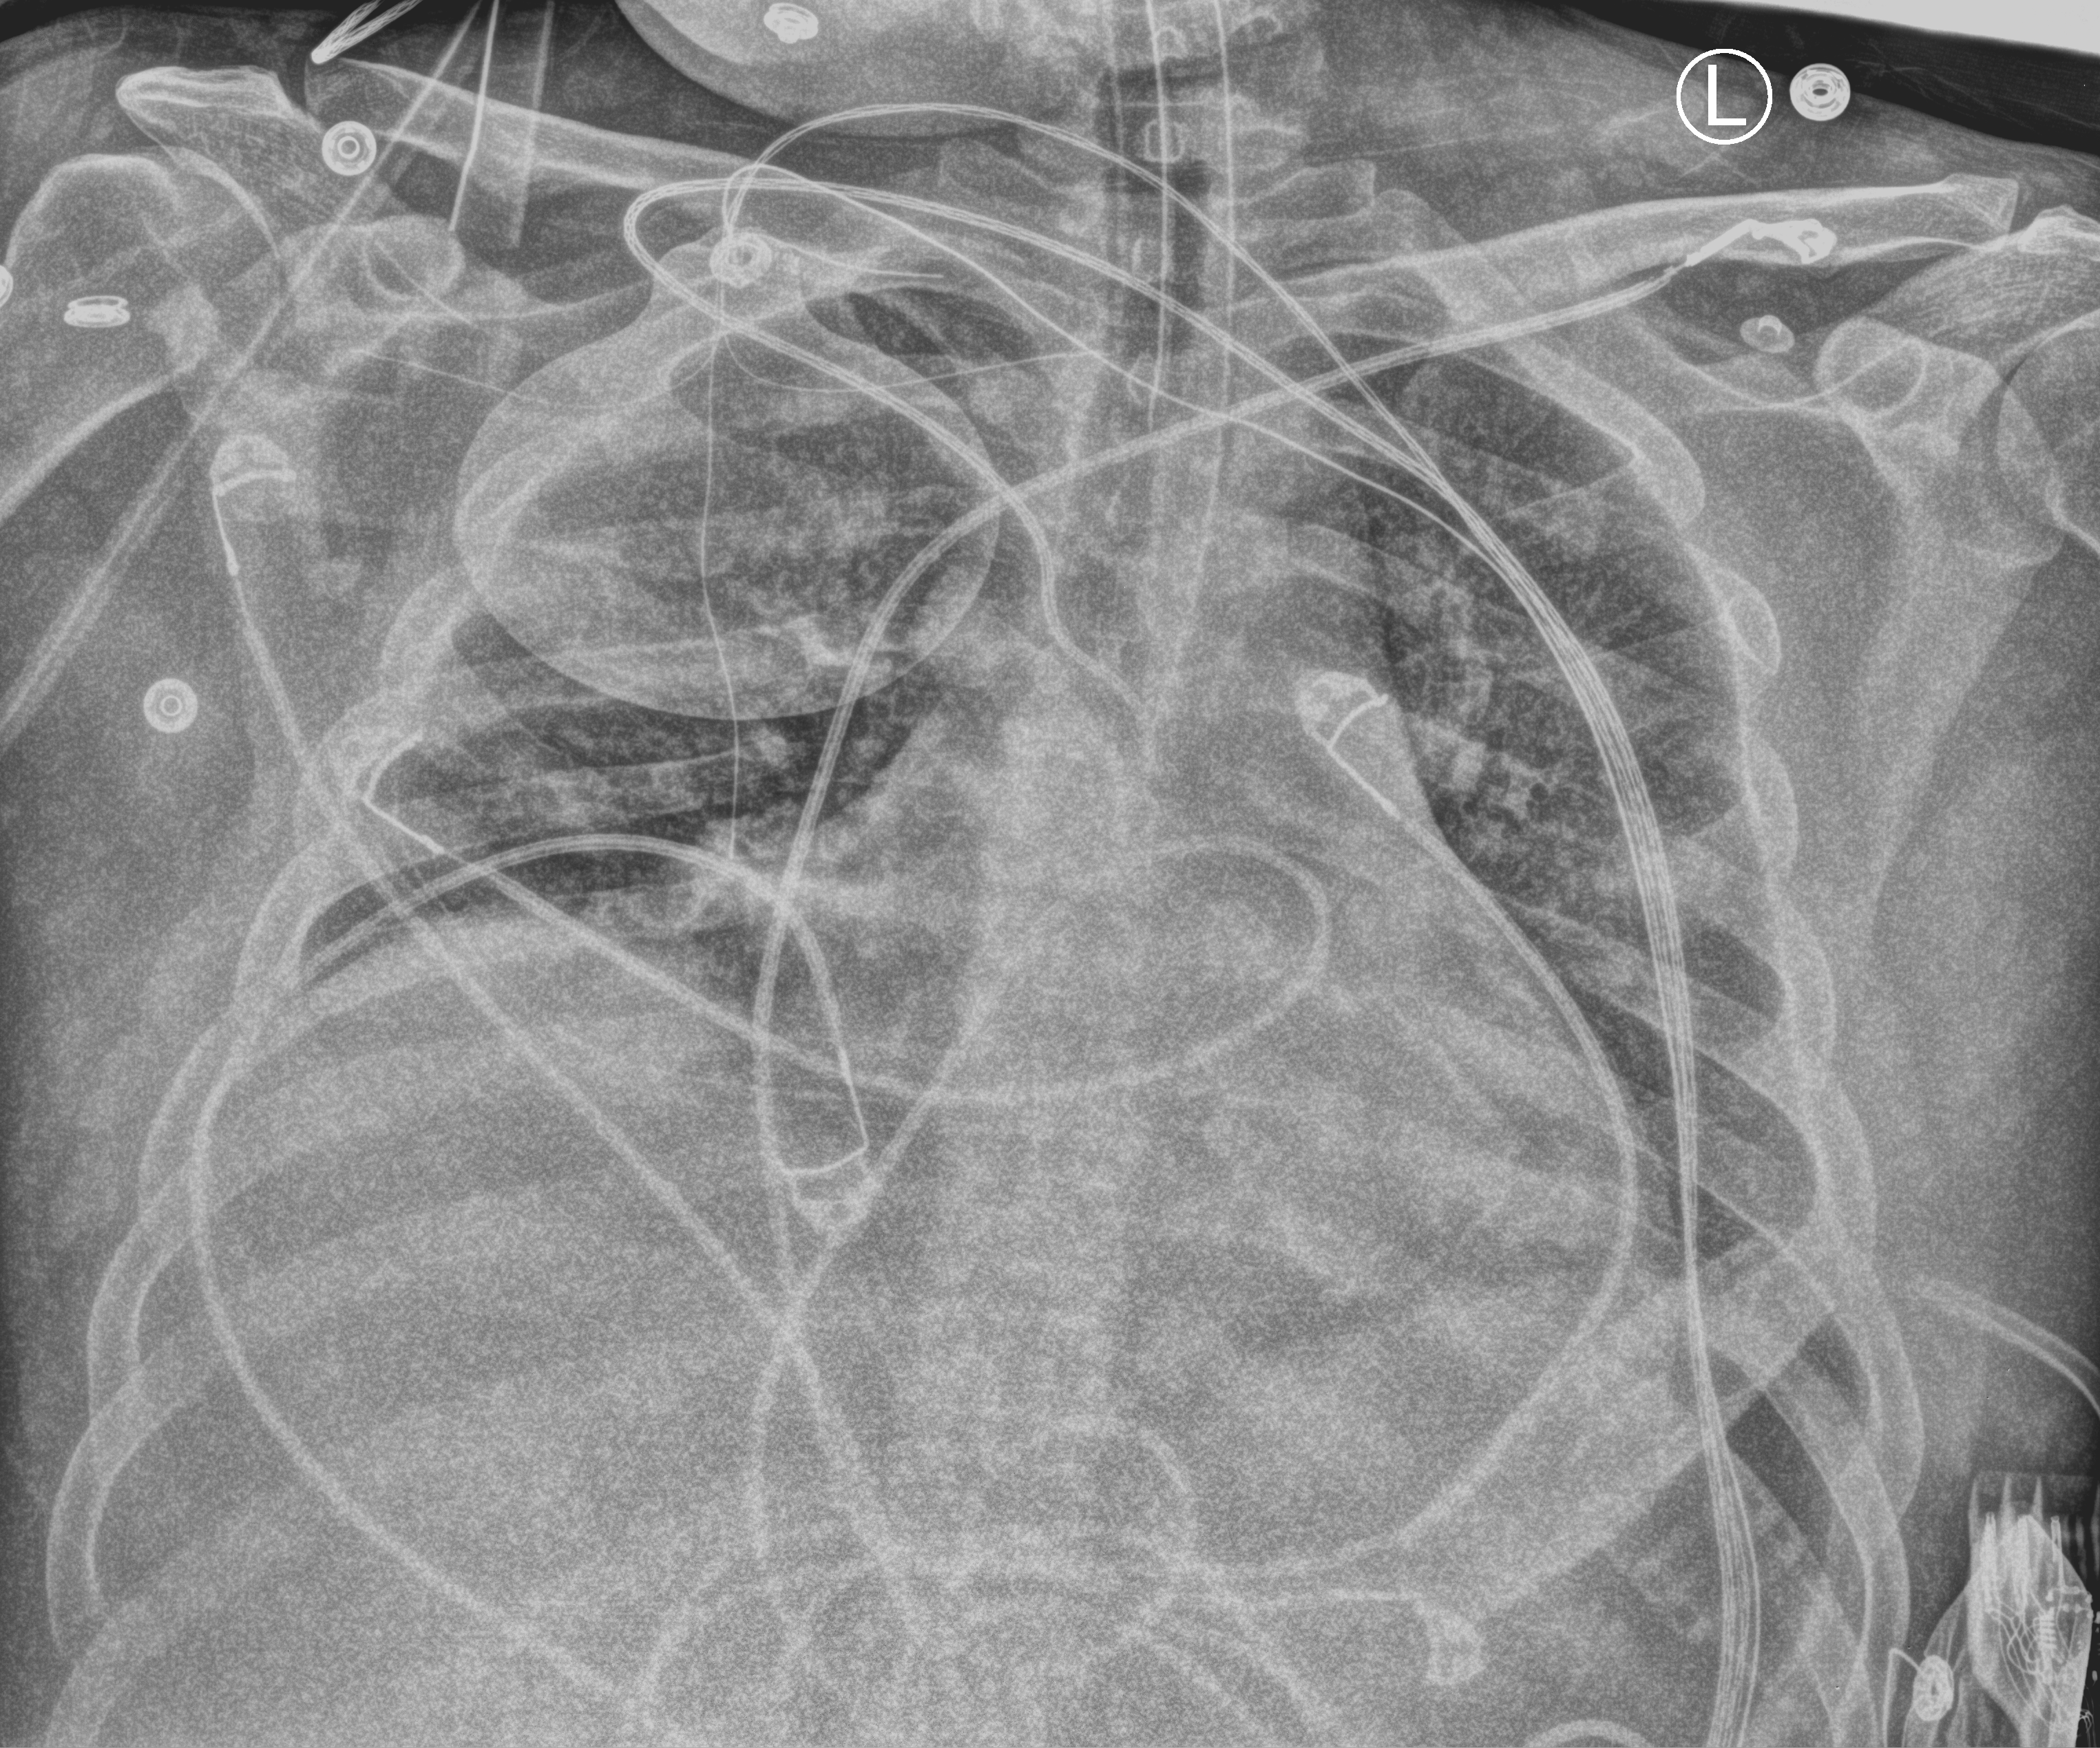
Bedside chest radiograph (computed radiography), anteroposterior (AP) projection. Male patient hospitalised with COVID-19, age 18–59 years.
From the hospital-stay record, not from the radiograph (when in the stay this image was taken is not recorded): COPD (admission record): no; mechanically ventilated during this hospital stay: yes; length of hospital stay: 61 days.